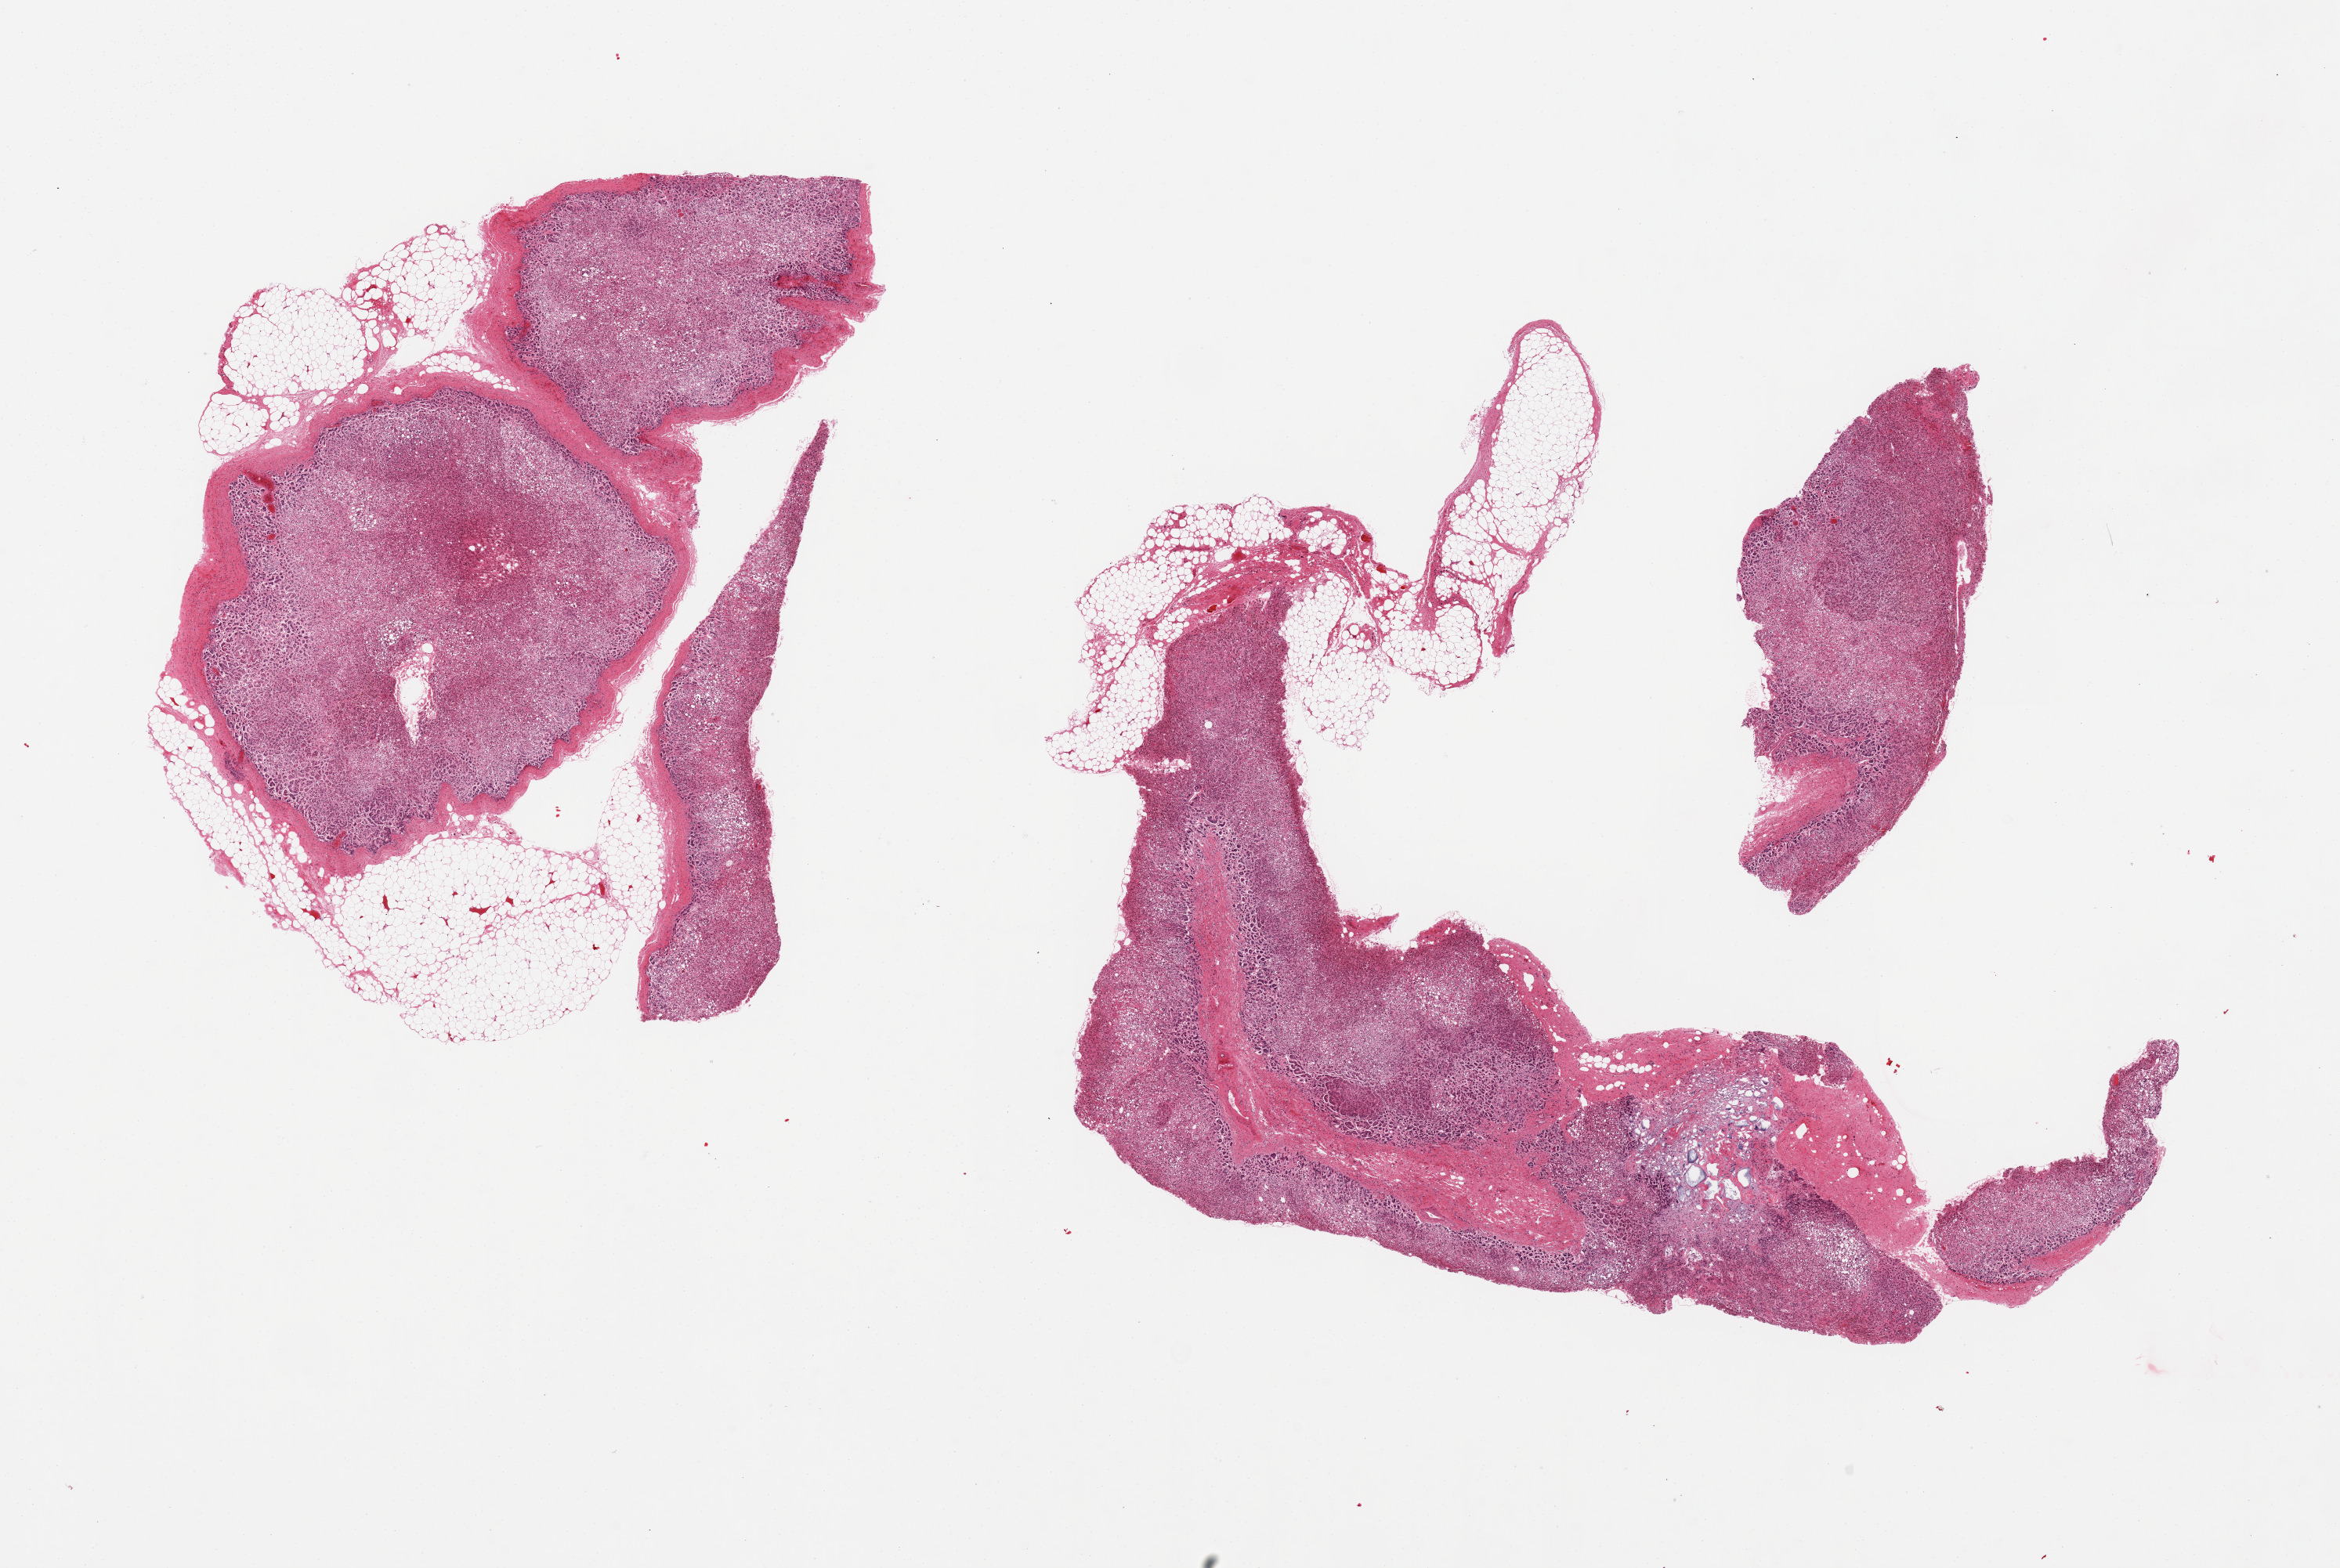
Whole-slide image, hematoxylin and eosin (H&E) stain, brightfield, low-resolution overview of the scanned area, about 23.6 x 15.8 mm. PAXgene-fixed, paraffin-embedded tissue. Target tissue: adrenal gland. Donor tissue sample. Donor sex: male.
Reviewer comment on this tissue sample: 2 pieces with fragments; (benign) adenomatoid tumor; 30% peripheral fat.